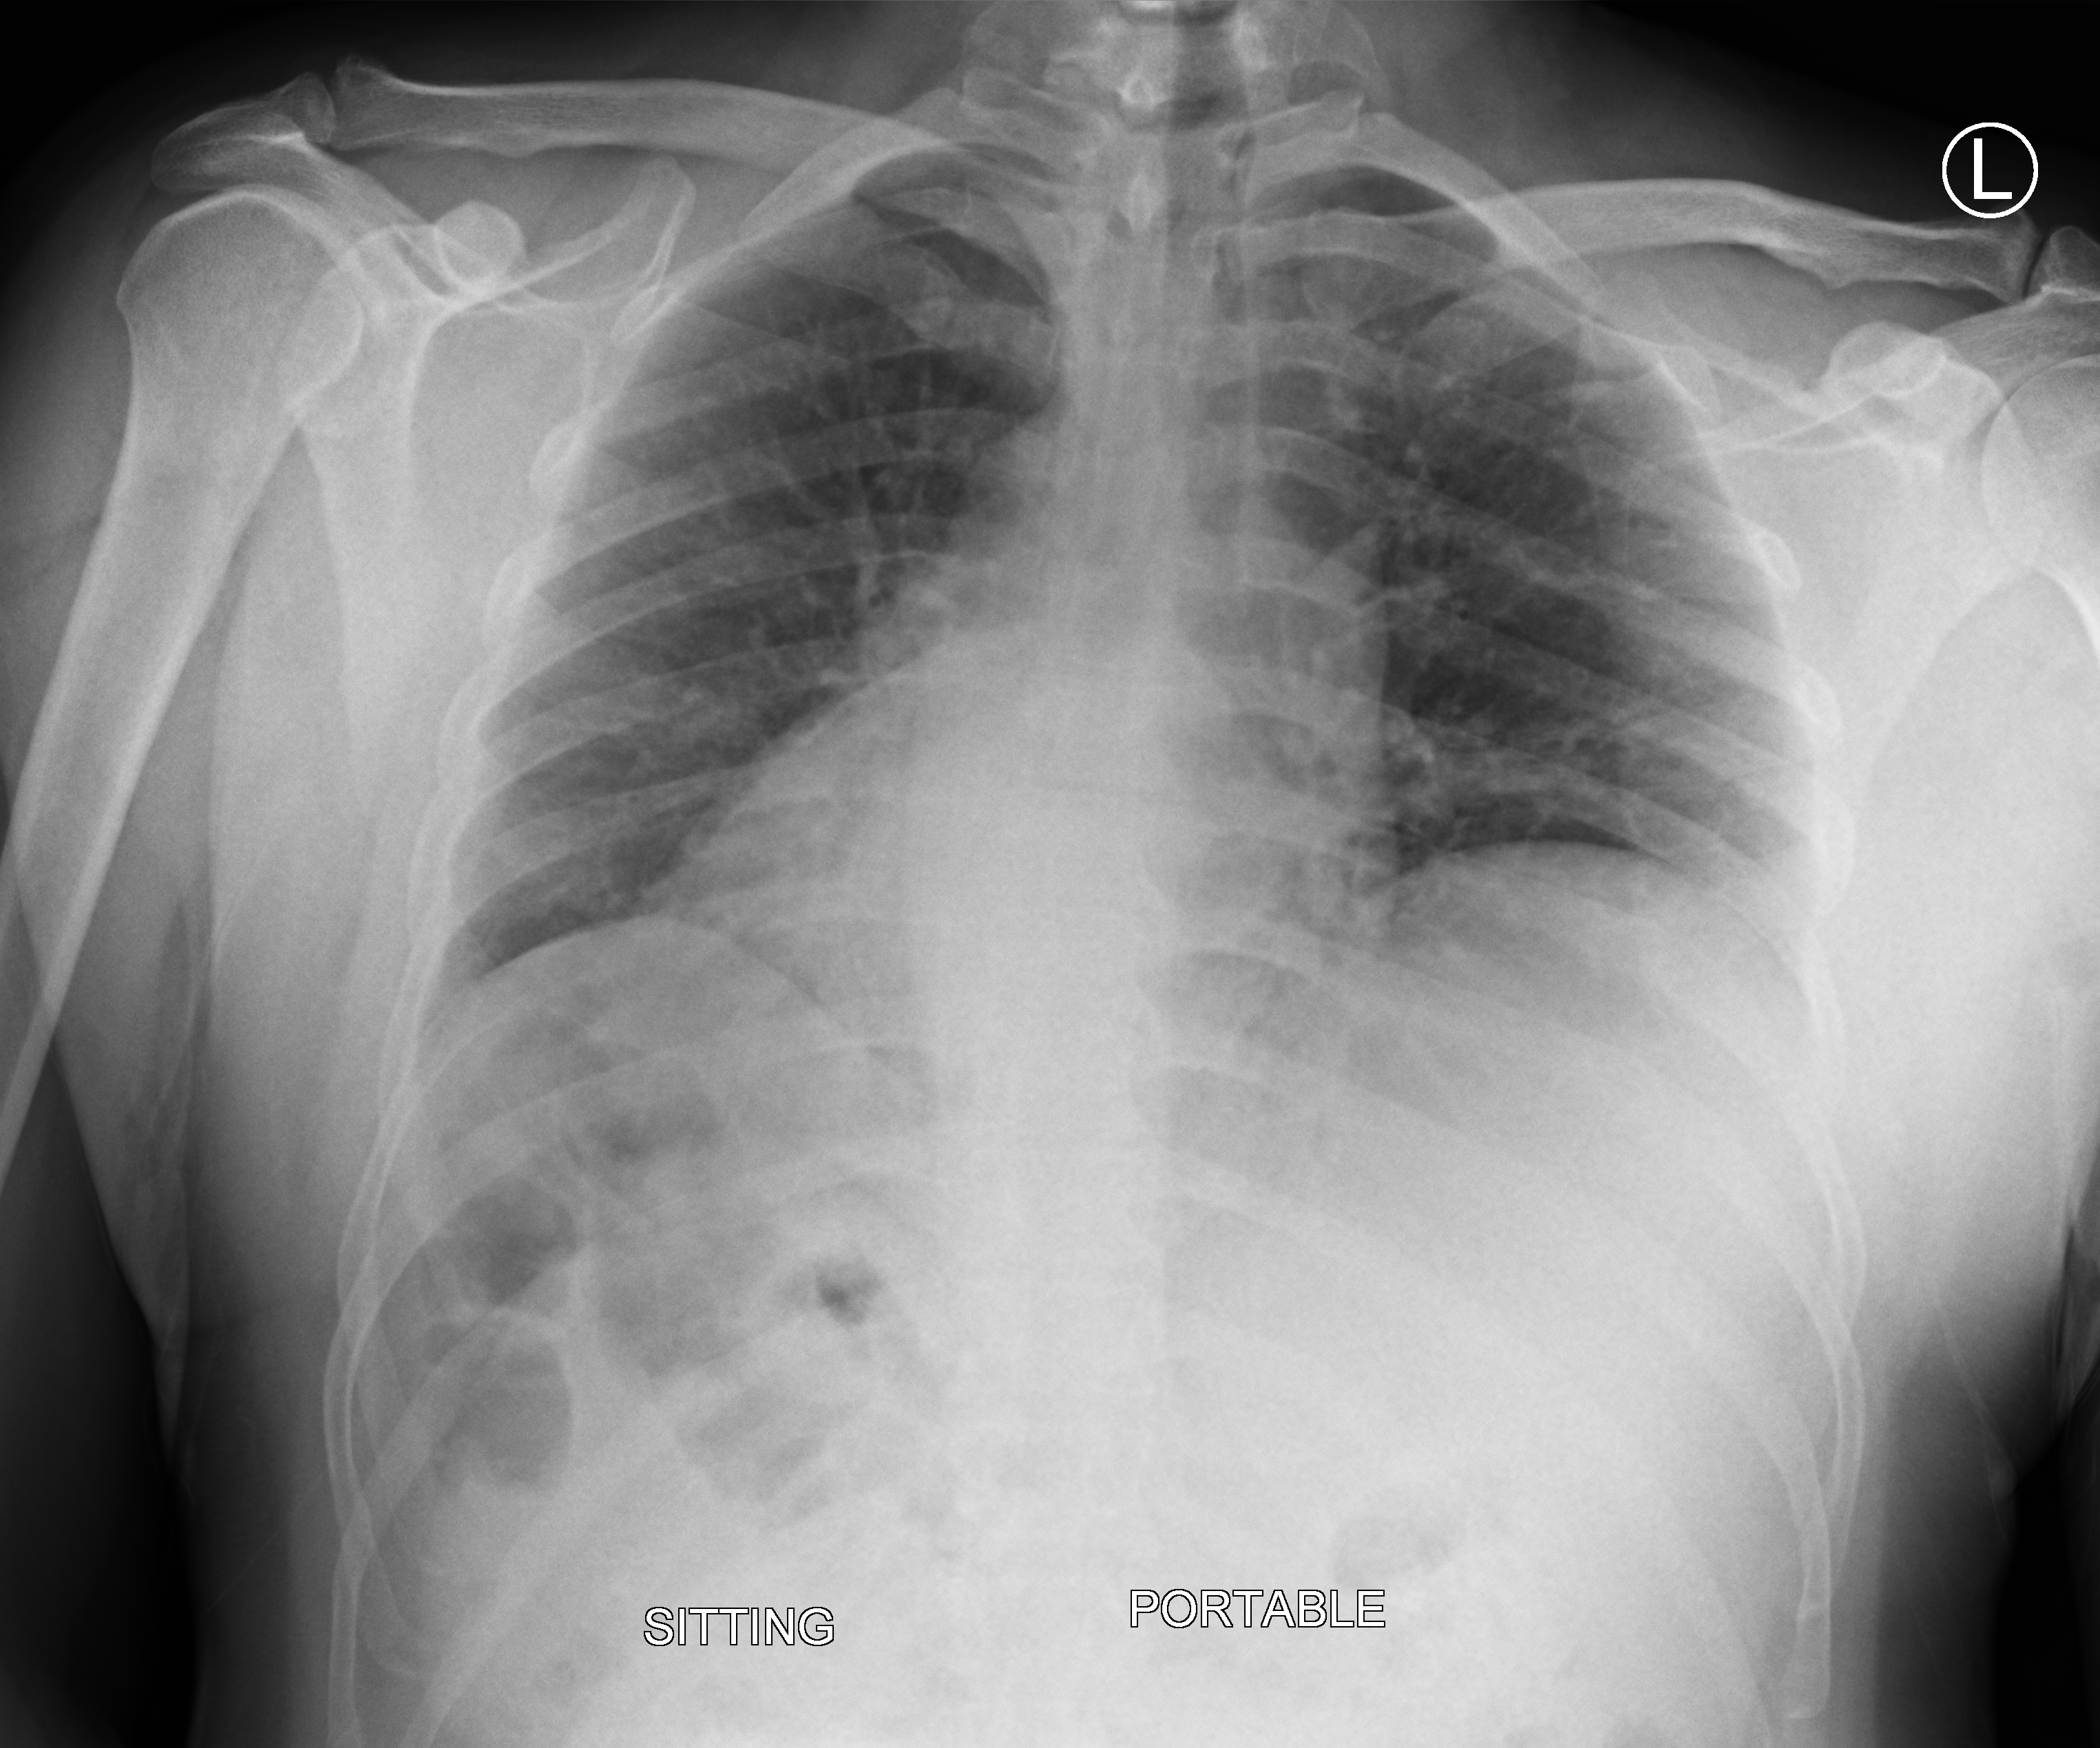
Chest X-ray (portable), anteroposterior (AP) projection. Male patient hospitalised with COVID-19, age 18–59 years.
From the hospital-stay record, not from the radiograph (when in the stay this image was taken is not recorded): smoking status (admission record): never.